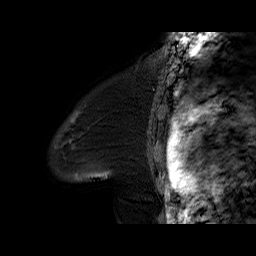
Breast MRI (dynamic contrast-enhanced), one sagittal slice; position 52 of 60 along the scan axis; dynamic contrast-enhanced series, time point 2 of 6 at this slice position (early post-contrast); 1.5 T; TE 6.2 ms, TR 32.4 ms; 4 mm slice thickness; 256 × 256 image matrix. Female patient. From the clinical record (not read from this slice): setting: breast cancer imaged before/during neoadjuvant chemotherapy; receptor status: triple-negative.
Annotated regions visible in this slice (semi-automatically segmented with operator editing):
- analysis volume of interest (the breast-tissue region the enhancement analysis was run in; not a lesion): bounding box (x1, y1, x2, y2) in pixels: (51, 97, 134, 189)
- tumour enhancement mask (voxels above the 100 % enhancement threshold inside the analysis volume of interest): (75, 175, 77, 177)